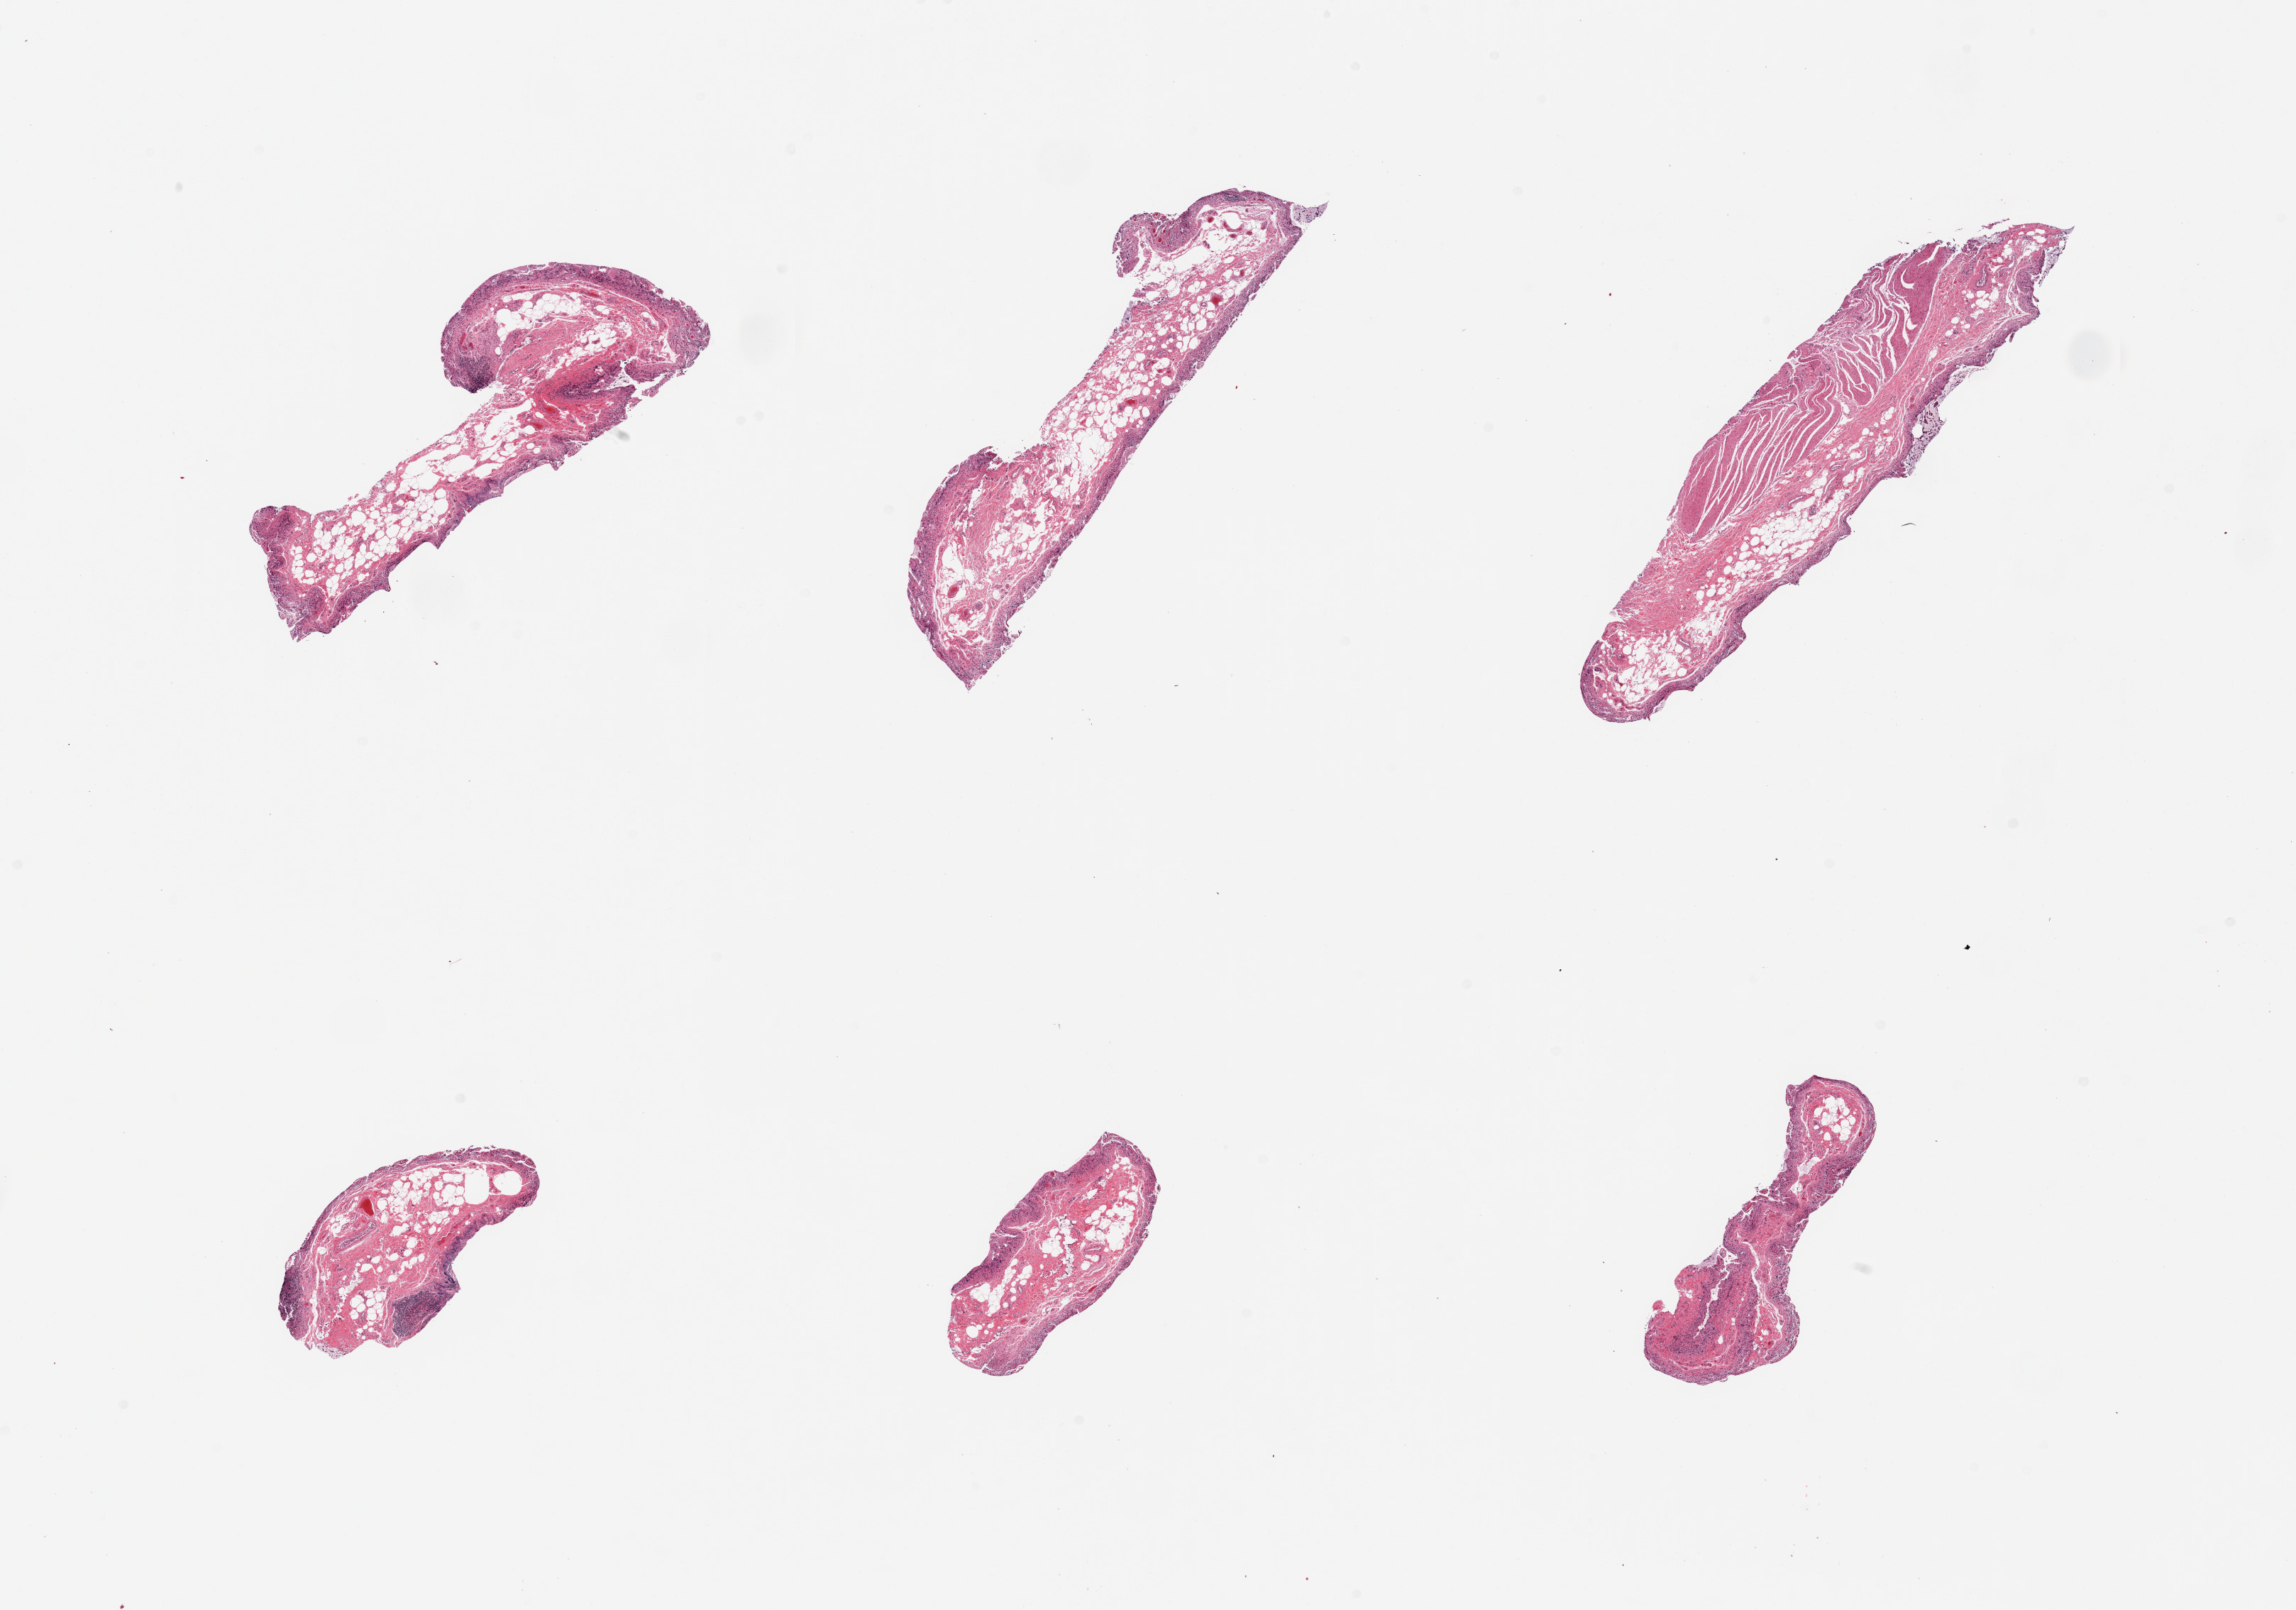
Digitized hematoxylin and eosin (H&E)-stained section, whole scanned area (about 25.6 x 17.9 mm) shown as a low-resolution overview, PAXgene-fixed, paraffin-embedded tissue, section of ileum (target tissue), tissue donor sample.
Pathologist's review note for this sample: 6 pieces, totally autolyzed, less than 5% lympohid elements.